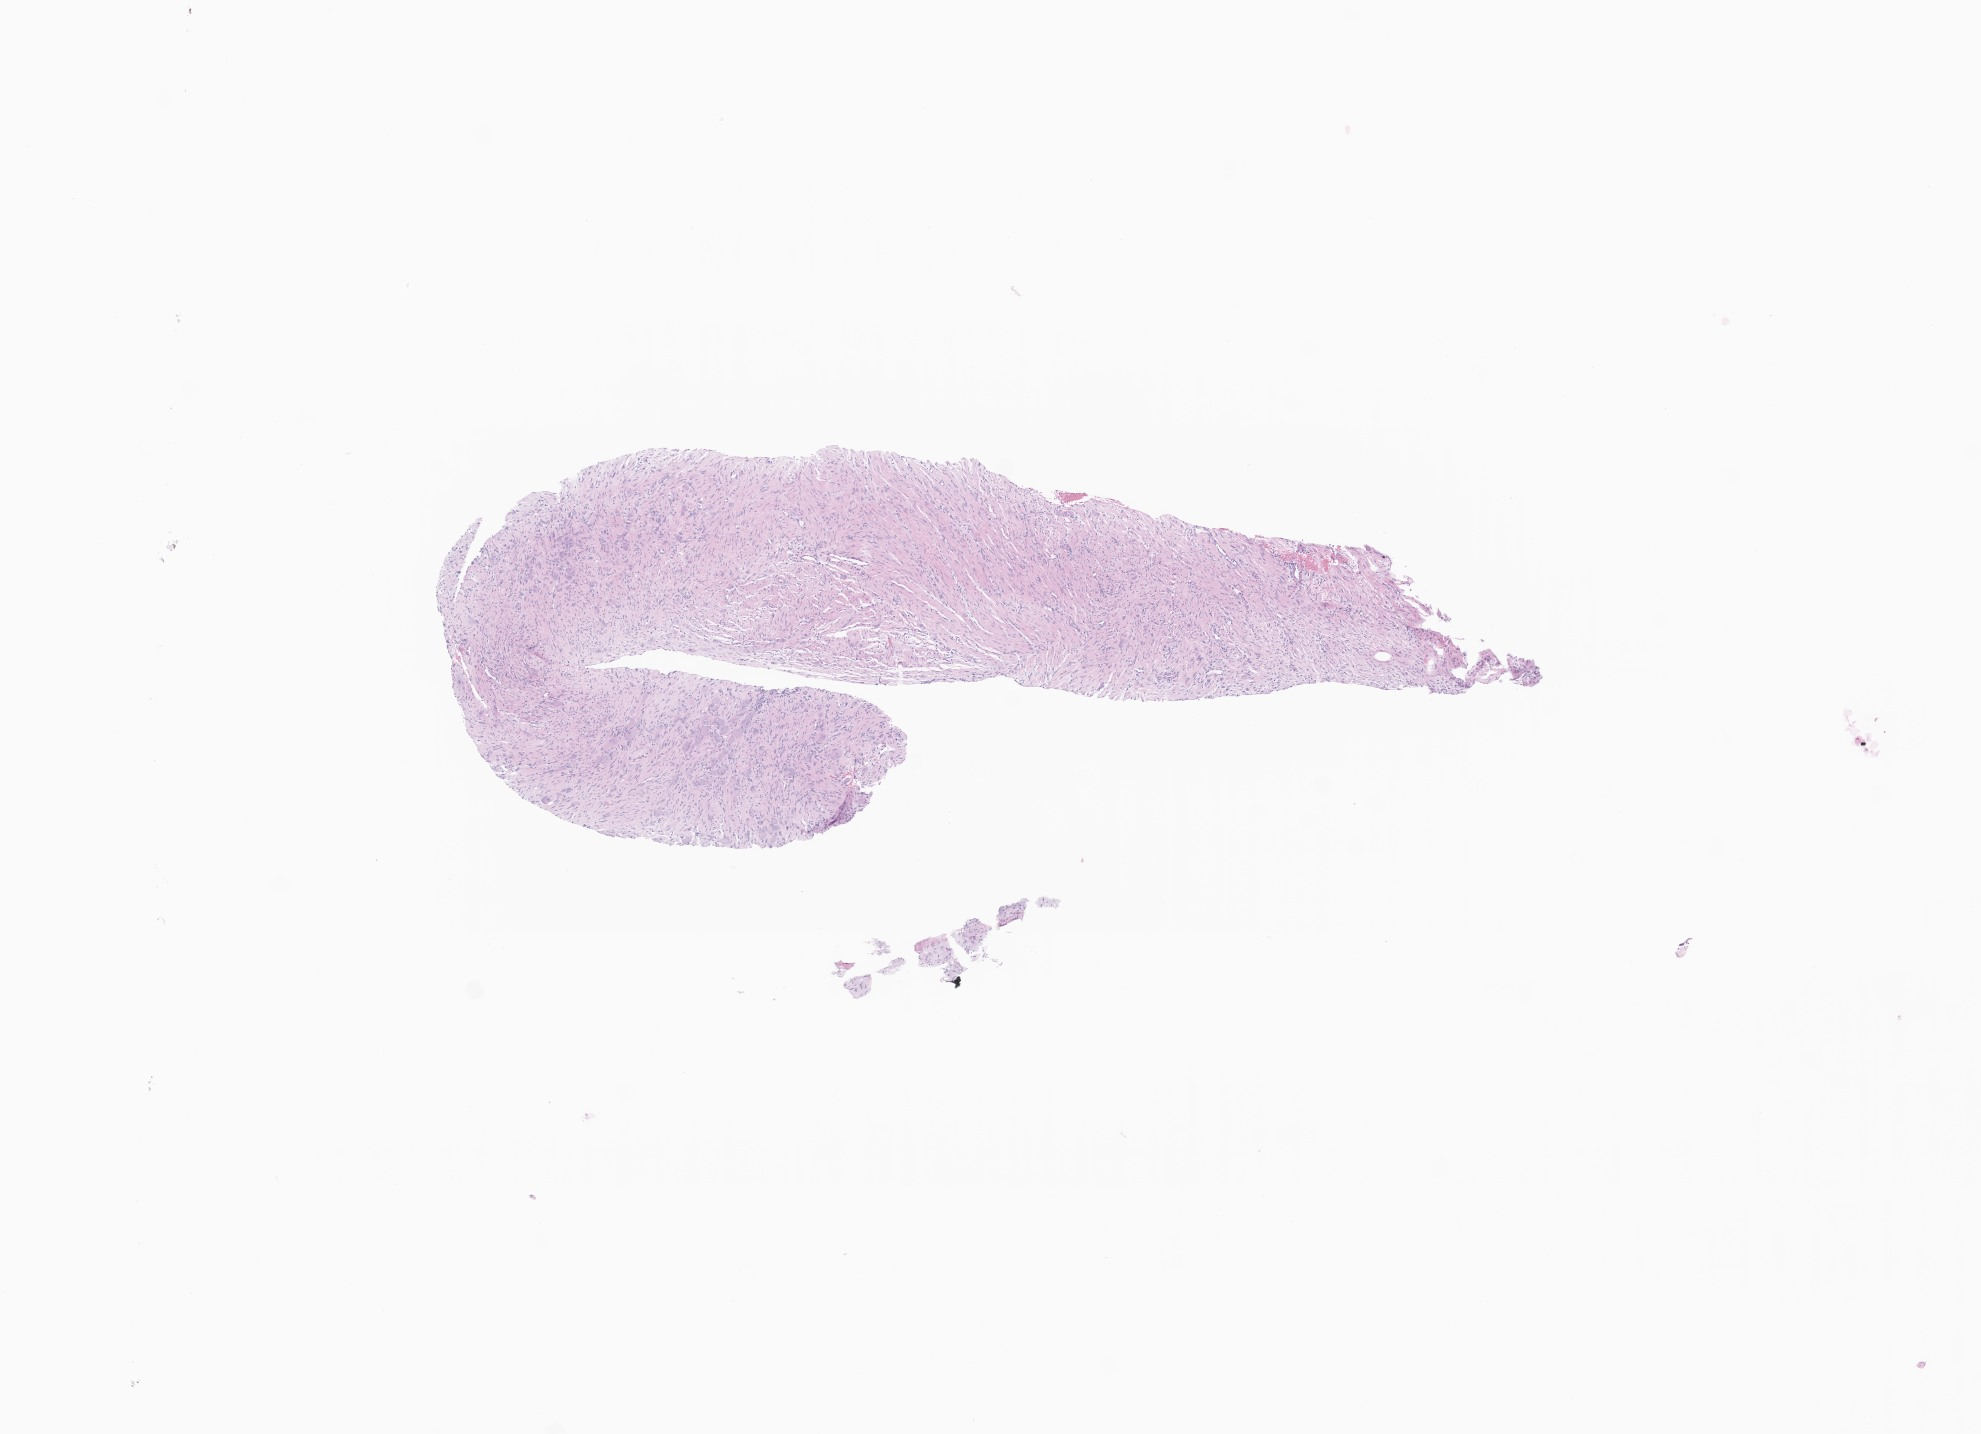
Whole-slide image, haematoxylin and eosin stain of tumor tissue from the adrenal gland, whole scanned area (about 8.4 x 6.0 mm) shown as a low-resolution overview; FFPE section. Male patient, age 97 months.
Recorded diagnosis: Ganglioneuroma.